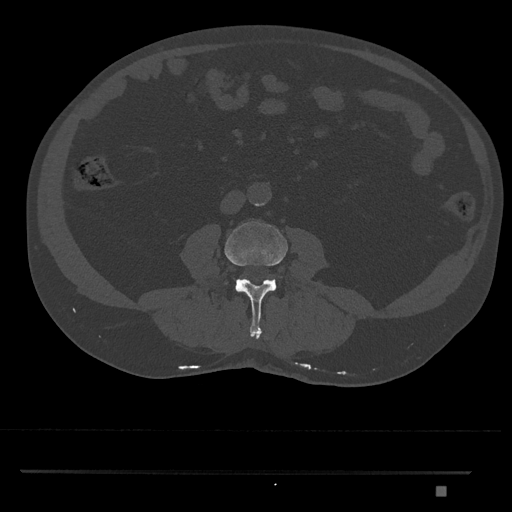
CT including the spine, one axial slice. Slice 671 of 1134 in the series (ordered by position). Reconstruction kernel Br40s/3. 120 kVp. Bone window (W 1800 / L 400 HU). 0.5 mm slice thickness. 512 × 512 image matrix. Male patient, age 65 years. Case-level facts recorded for this patient, not image findings: primary cancer: prostate.
Outlined on this slice (semi-automatically segmented with operator editing):
- L3 vertebra: bounding box <225,221,288,339> (left, top, right, bottom; pixels)